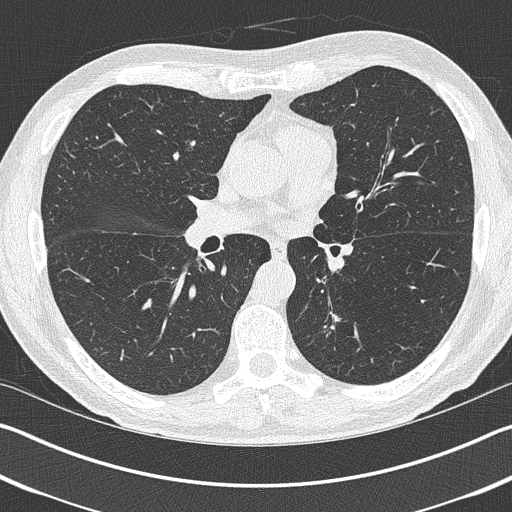
Axial slice from a low-dose chest CT screening exam; first (baseline) screen; lung window (W 1500 / L -600 HU); 1 mm slice thickness; 120 kVp; slice 179 of 402 in the series. Male participant, aged 69 years at enrolment. Current smoker at enrolment.
• Expert-annotated lung lesion, box from (x=292, y=304) to (x=349, y=364) px.
• The exam's reader record, not a measurement of the box and not confirmed to be the same lesion: non-calcified nodule or mass ≥4 mm, left upper lobe, 19 × 19 mm, spiculated (stellate) margins, pre-existing on the prior screen: yes.
• Official screen result: positive, change unspecified: nodule(s) >= 4 mm or enlarging nodule(s), mass(es), or other non-specific abnormalities suspicious for lung cancer.
• Lung cancer was diagnosed 202 days after this screen: non-small cell carcinoma, left lower lobe, stage IIIA (AJCC 6th edition), 20 mm at pathology.